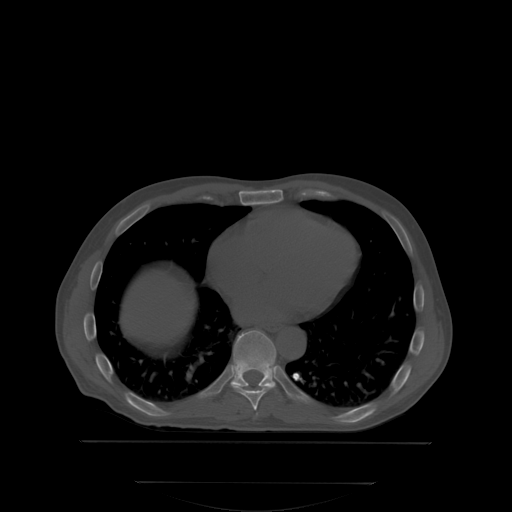
CT including the spine, one axial slice. Slice 210 of 350 in the series (ordered by position). Bone window (W 1800 / L 400 HU). 2.5 mm slice thickness. 512 × 512 image matrix, field of view 500 × 500 mm. Patient: male, 58 years. Case-level facts recorded for this patient, not image findings: primary cancer: prostate; vertebrae with lytic lesions (as recorded): L1.
Annotated regions visible in this slice (semi-automatic segmentation, software-assisted and operator-edited):
- T8 vertebra: bounding box (x1, y1, x2, y2) in pixels: (231, 369, 277, 411)
- T9 vertebra: (230, 330, 276, 388)